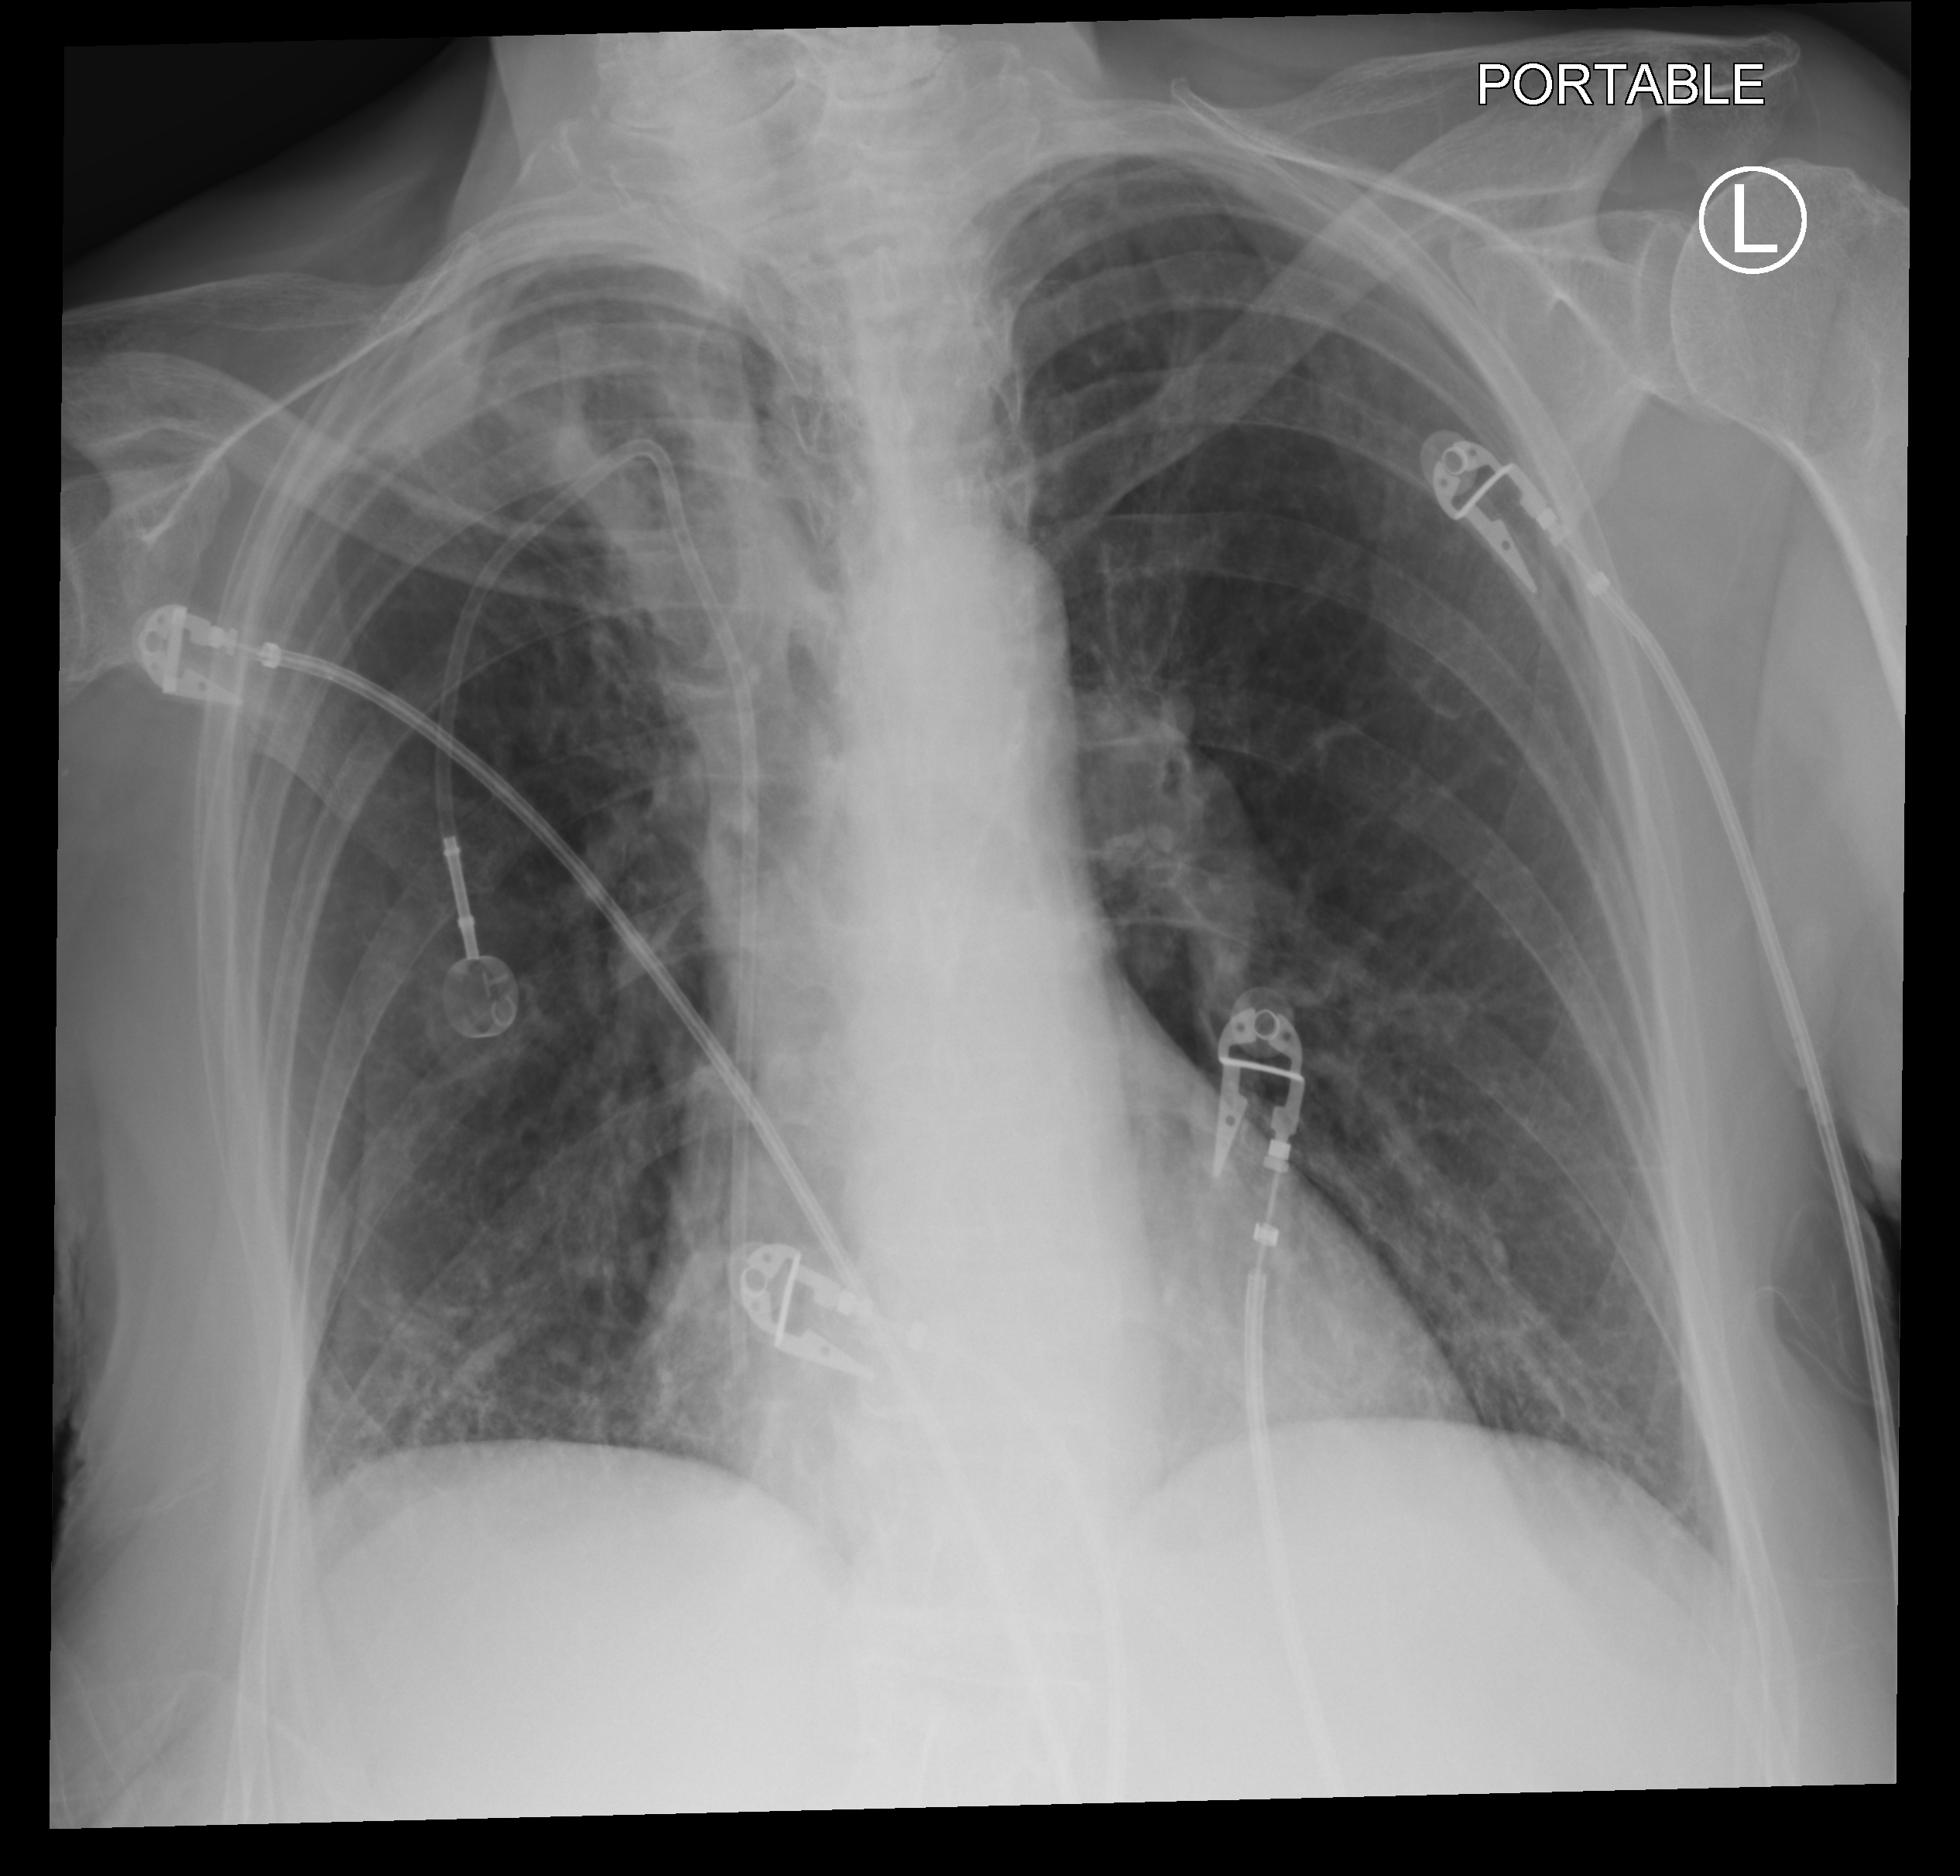
Portable chest radiograph, anteroposterior (AP) projection. Patient hospitalised with COVID-19; female, aged 60–74 years.
From the hospital-stay record, not from the radiograph (when in the stay this image was taken is not recorded): mechanically ventilated during this hospital stay: no; admitted to intensive care during this hospital stay: no.